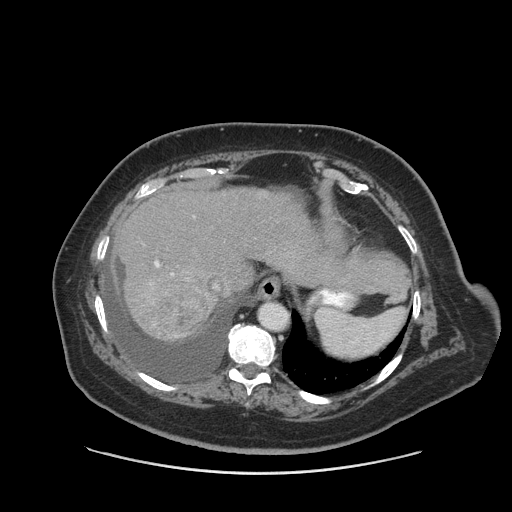
Contrast-enhanced abdominal CT (liver protocol), one axial slice; position 68 of 91 along the scan axis; 140 kVp; soft-tissue window (W 400 / L 40 HU); 2.5 mm slice thickness; 512 × 512 image matrix, field of view 420 × 420 mm. Case-level facts recorded for this patient, not image findings: diagnosis: hepatocellular carcinoma (patient treated with transarterial chemoembolisation; whether this scan precedes or follows treatment is not stated here); TNM stage (as recorded): Stage-I; Child-Pugh class: A; tumour differentiation: well differentiated.
Structures marked on this image (semi-automatic segmentation, software-assisted and operator-edited):
- liver parenchyma outside the tumour (the mass and vessels are separate outlines, so this box may not span the whole liver): bounding box <114,184,330,340> (left, top, right, bottom; pixels)
- mass: <141,291,210,339>
- liver vessels: <154,261,173,275>